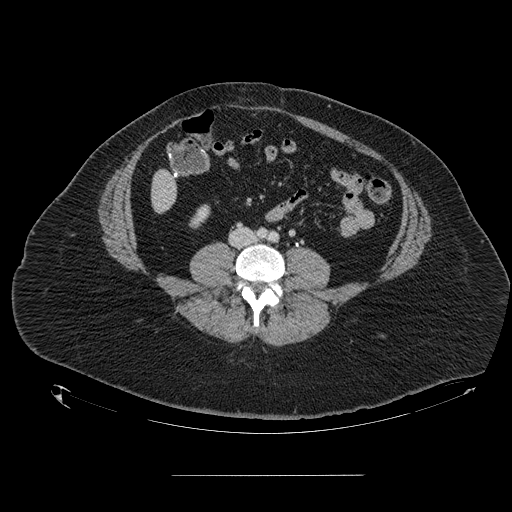
Contrast-enhanced abdominal CT, one axial slice. Slice 13 of 164 in the series (ordered by position). Intravenous contrast given. Soft-tissue window (W 400 / L 40 HU). 2.5 mm slice thickness. 512 × 512 image matrix. Female patient, age 52 years. From the clinical record (not read from this slice): diagnosis: colorectal cancer liver metastases, imaged before liver resection; multiple liver metastases: yes; largest metastasis: 3.5 cm; disease in both lobes: no.
Annotated regions visible in this slice (outlined manually by an expert reader):
- liver: bounding box (x1, y1, x2, y2) in pixels: (152, 172, 177, 212)